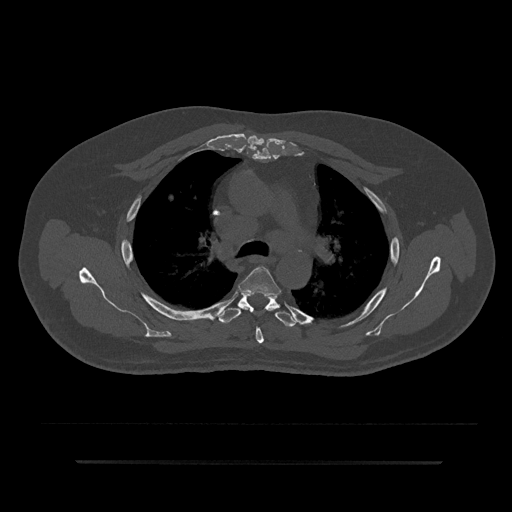
CT including the spine, one axial slice; position 597 of 797 along the scan axis; 120 kVp; bone window (W 1800 / L 400 HU); 0.5 mm slice thickness; 512 × 512 image matrix, field of view 464 × 464 mm. Patient: male, 59 years. Case-level facts recorded for this patient, not image findings: primary cancer: bile ducts.
Outlined on this slice (semi-automatic segmentation, software-assisted and operator-edited):
- T4 vertebra: box from (x=239, y=267) to (x=281, y=344) px
- T5 vertebra: (x=219, y=293)–(x=297, y=327)